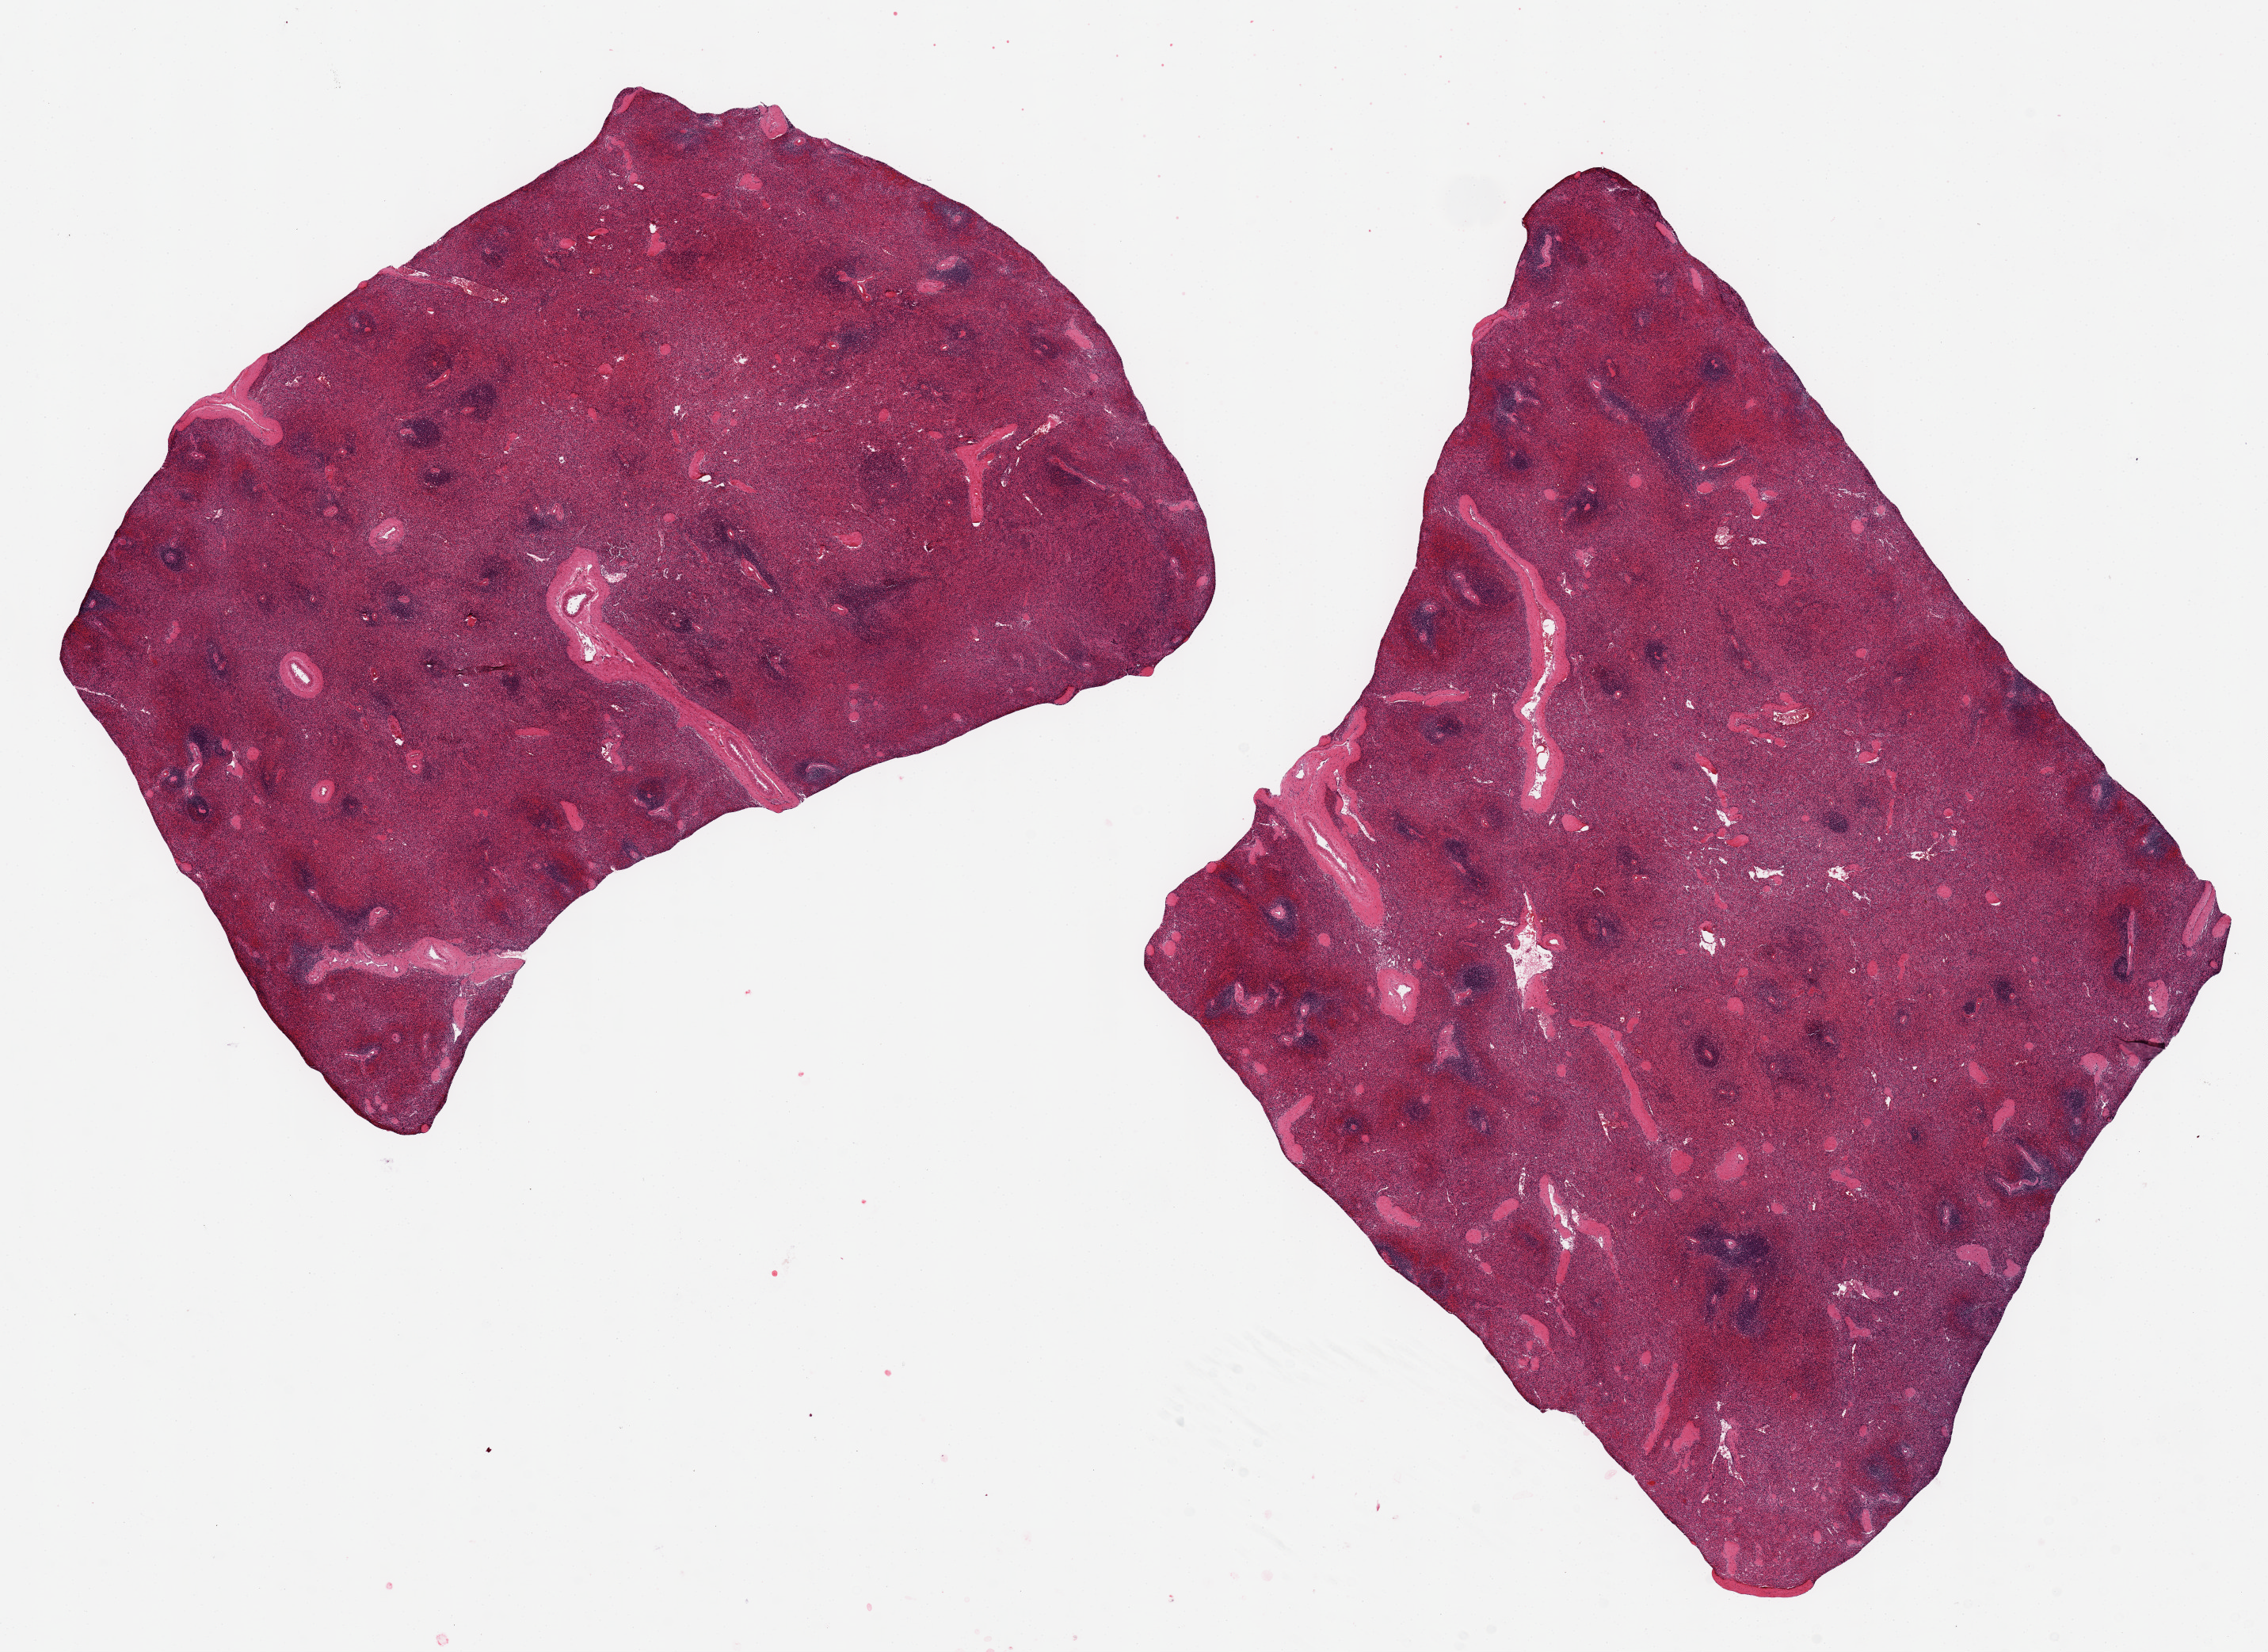
Digitized hematoxylin and eosin (H&E)-stained section, whole scanned area (about 22.6 x 16.5 mm, from a 20x scan) shown as a low-resolution overview. PAXgene-fixed paraffin-embedded (PFPE) section. Sampled site (target tissue): spleen. Tissue donor sample. Donor: male.
Review note (as recorded): 2 pieces ~10x8mm; slight congestion.